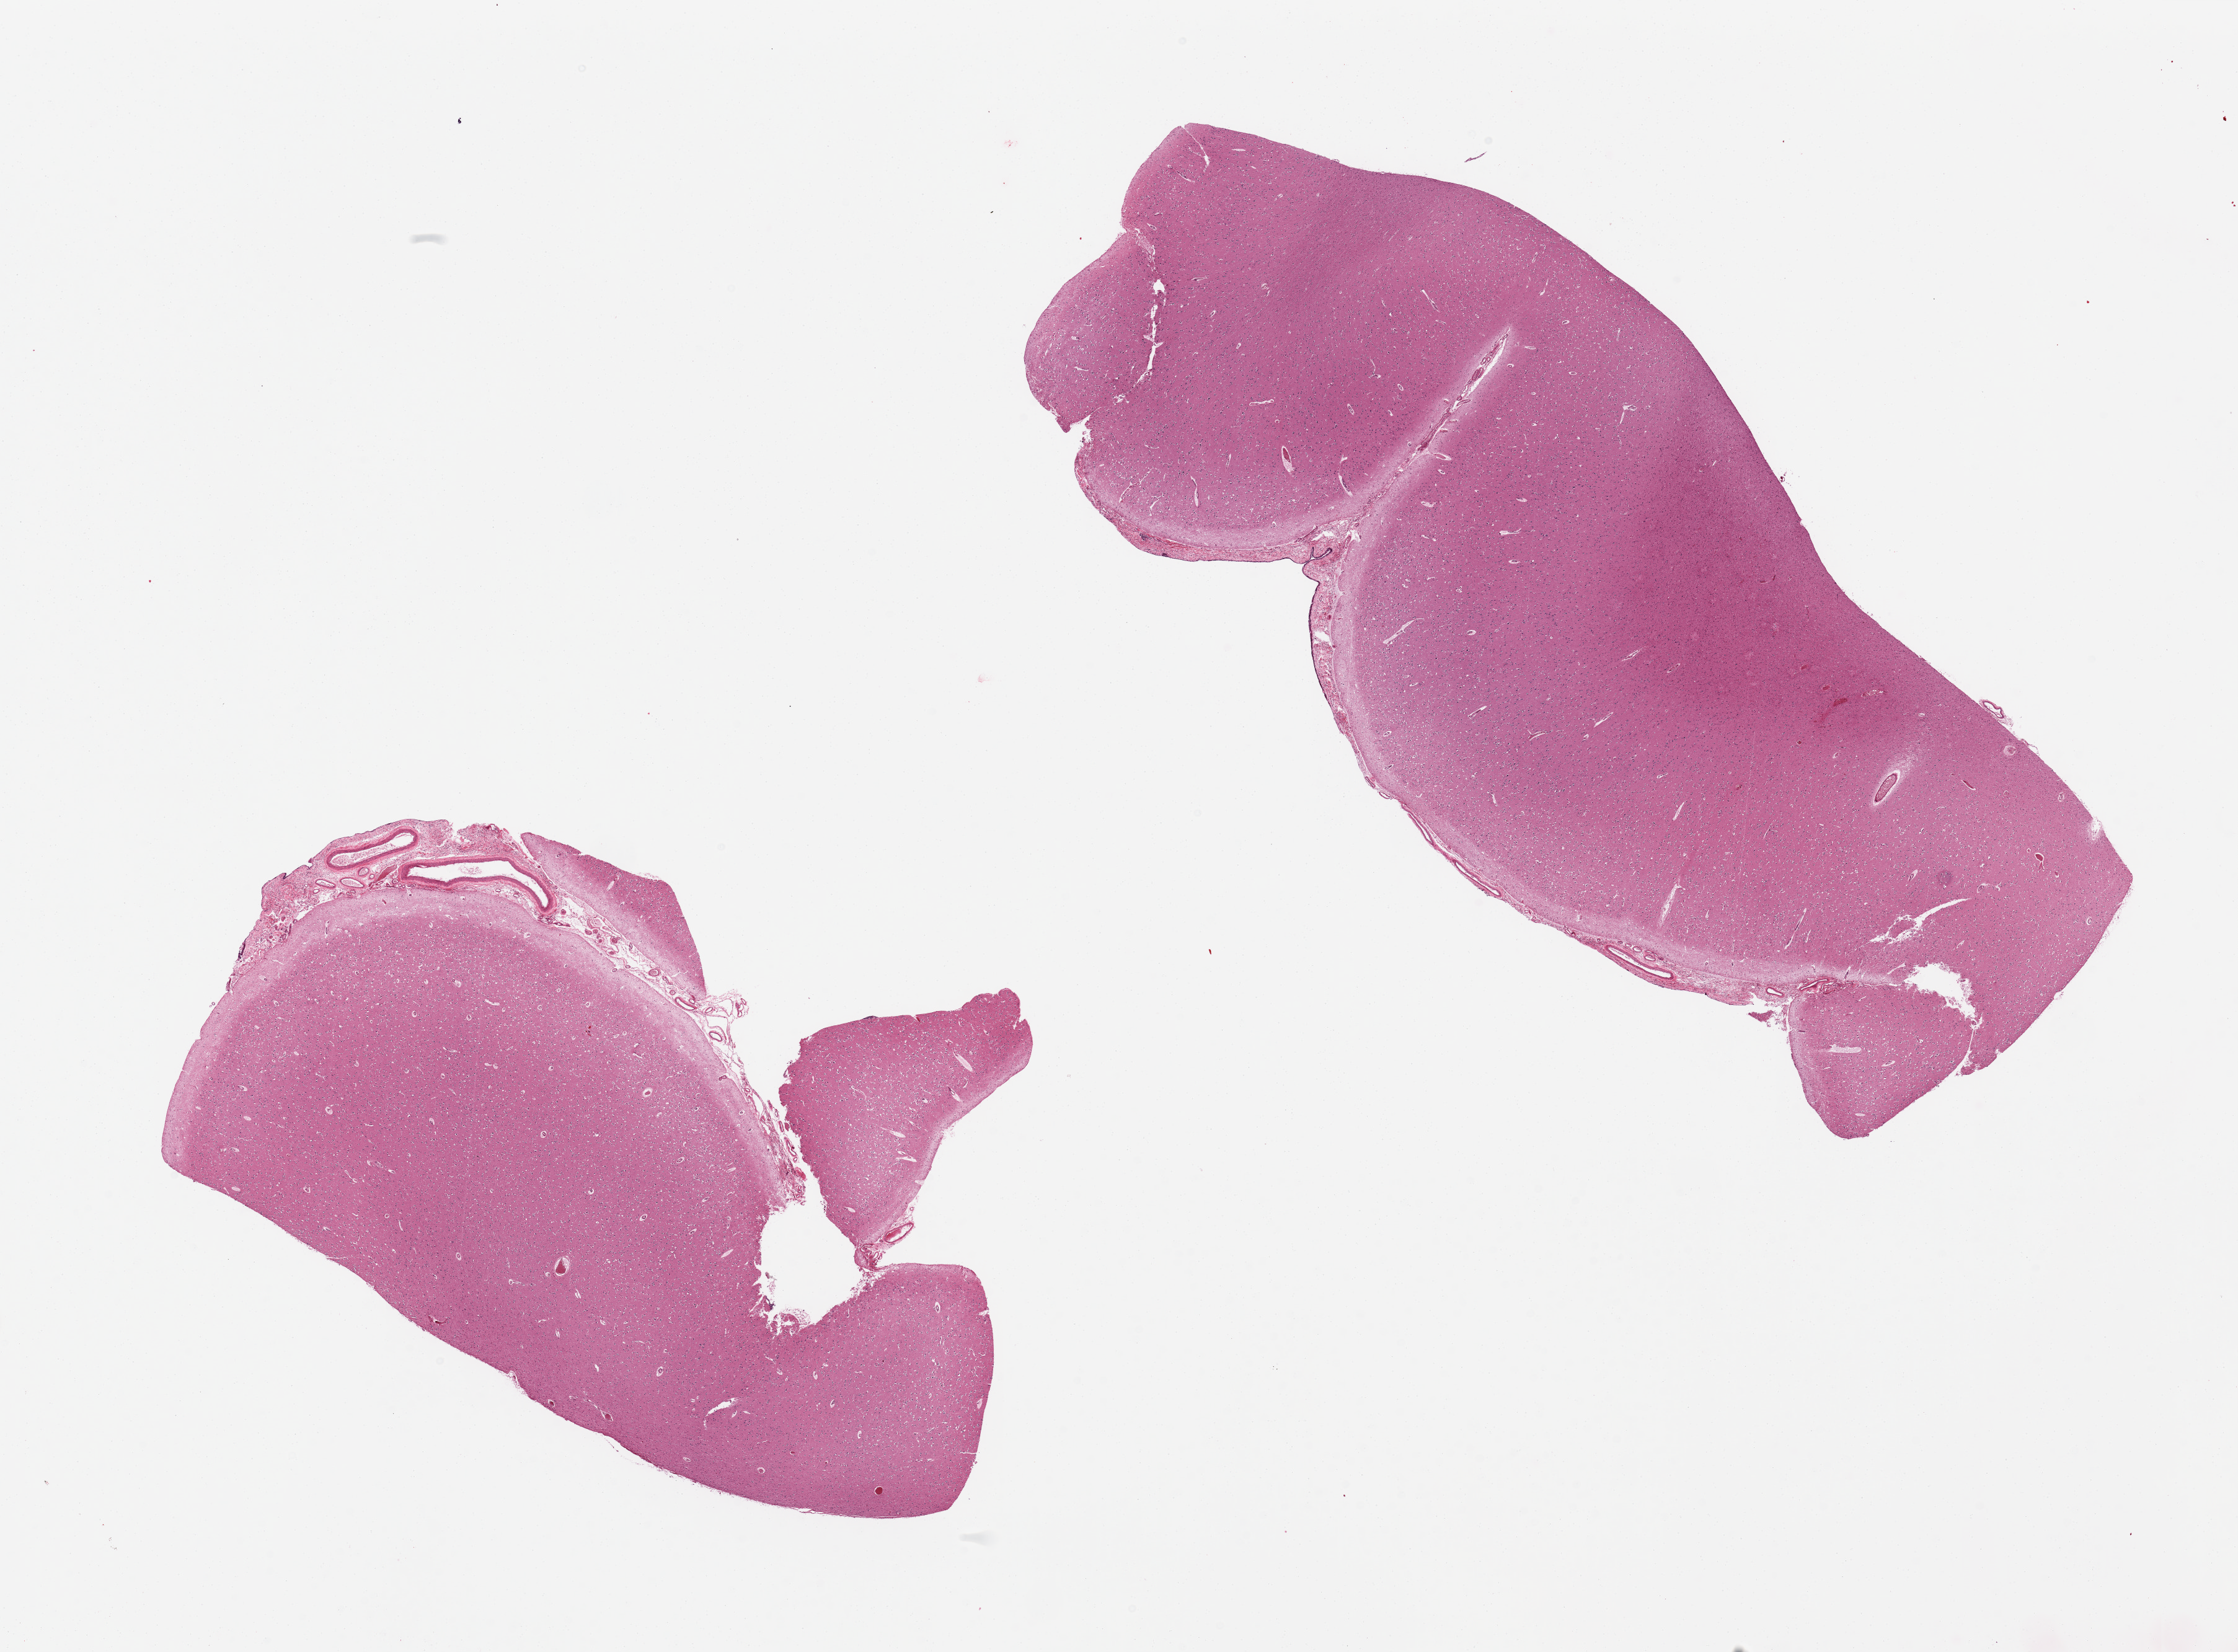
Digitized H&E-stained section, whole scanned area (about 28.5 x 21.1 mm) shown as a low-resolution overview. PAXgene-fixed, paraffin-embedded tissue. Target tissue: cerebral cortex. Tissue donor sample.
- reviewer comment on this tissue sample: 2 pieces, adherent meninges